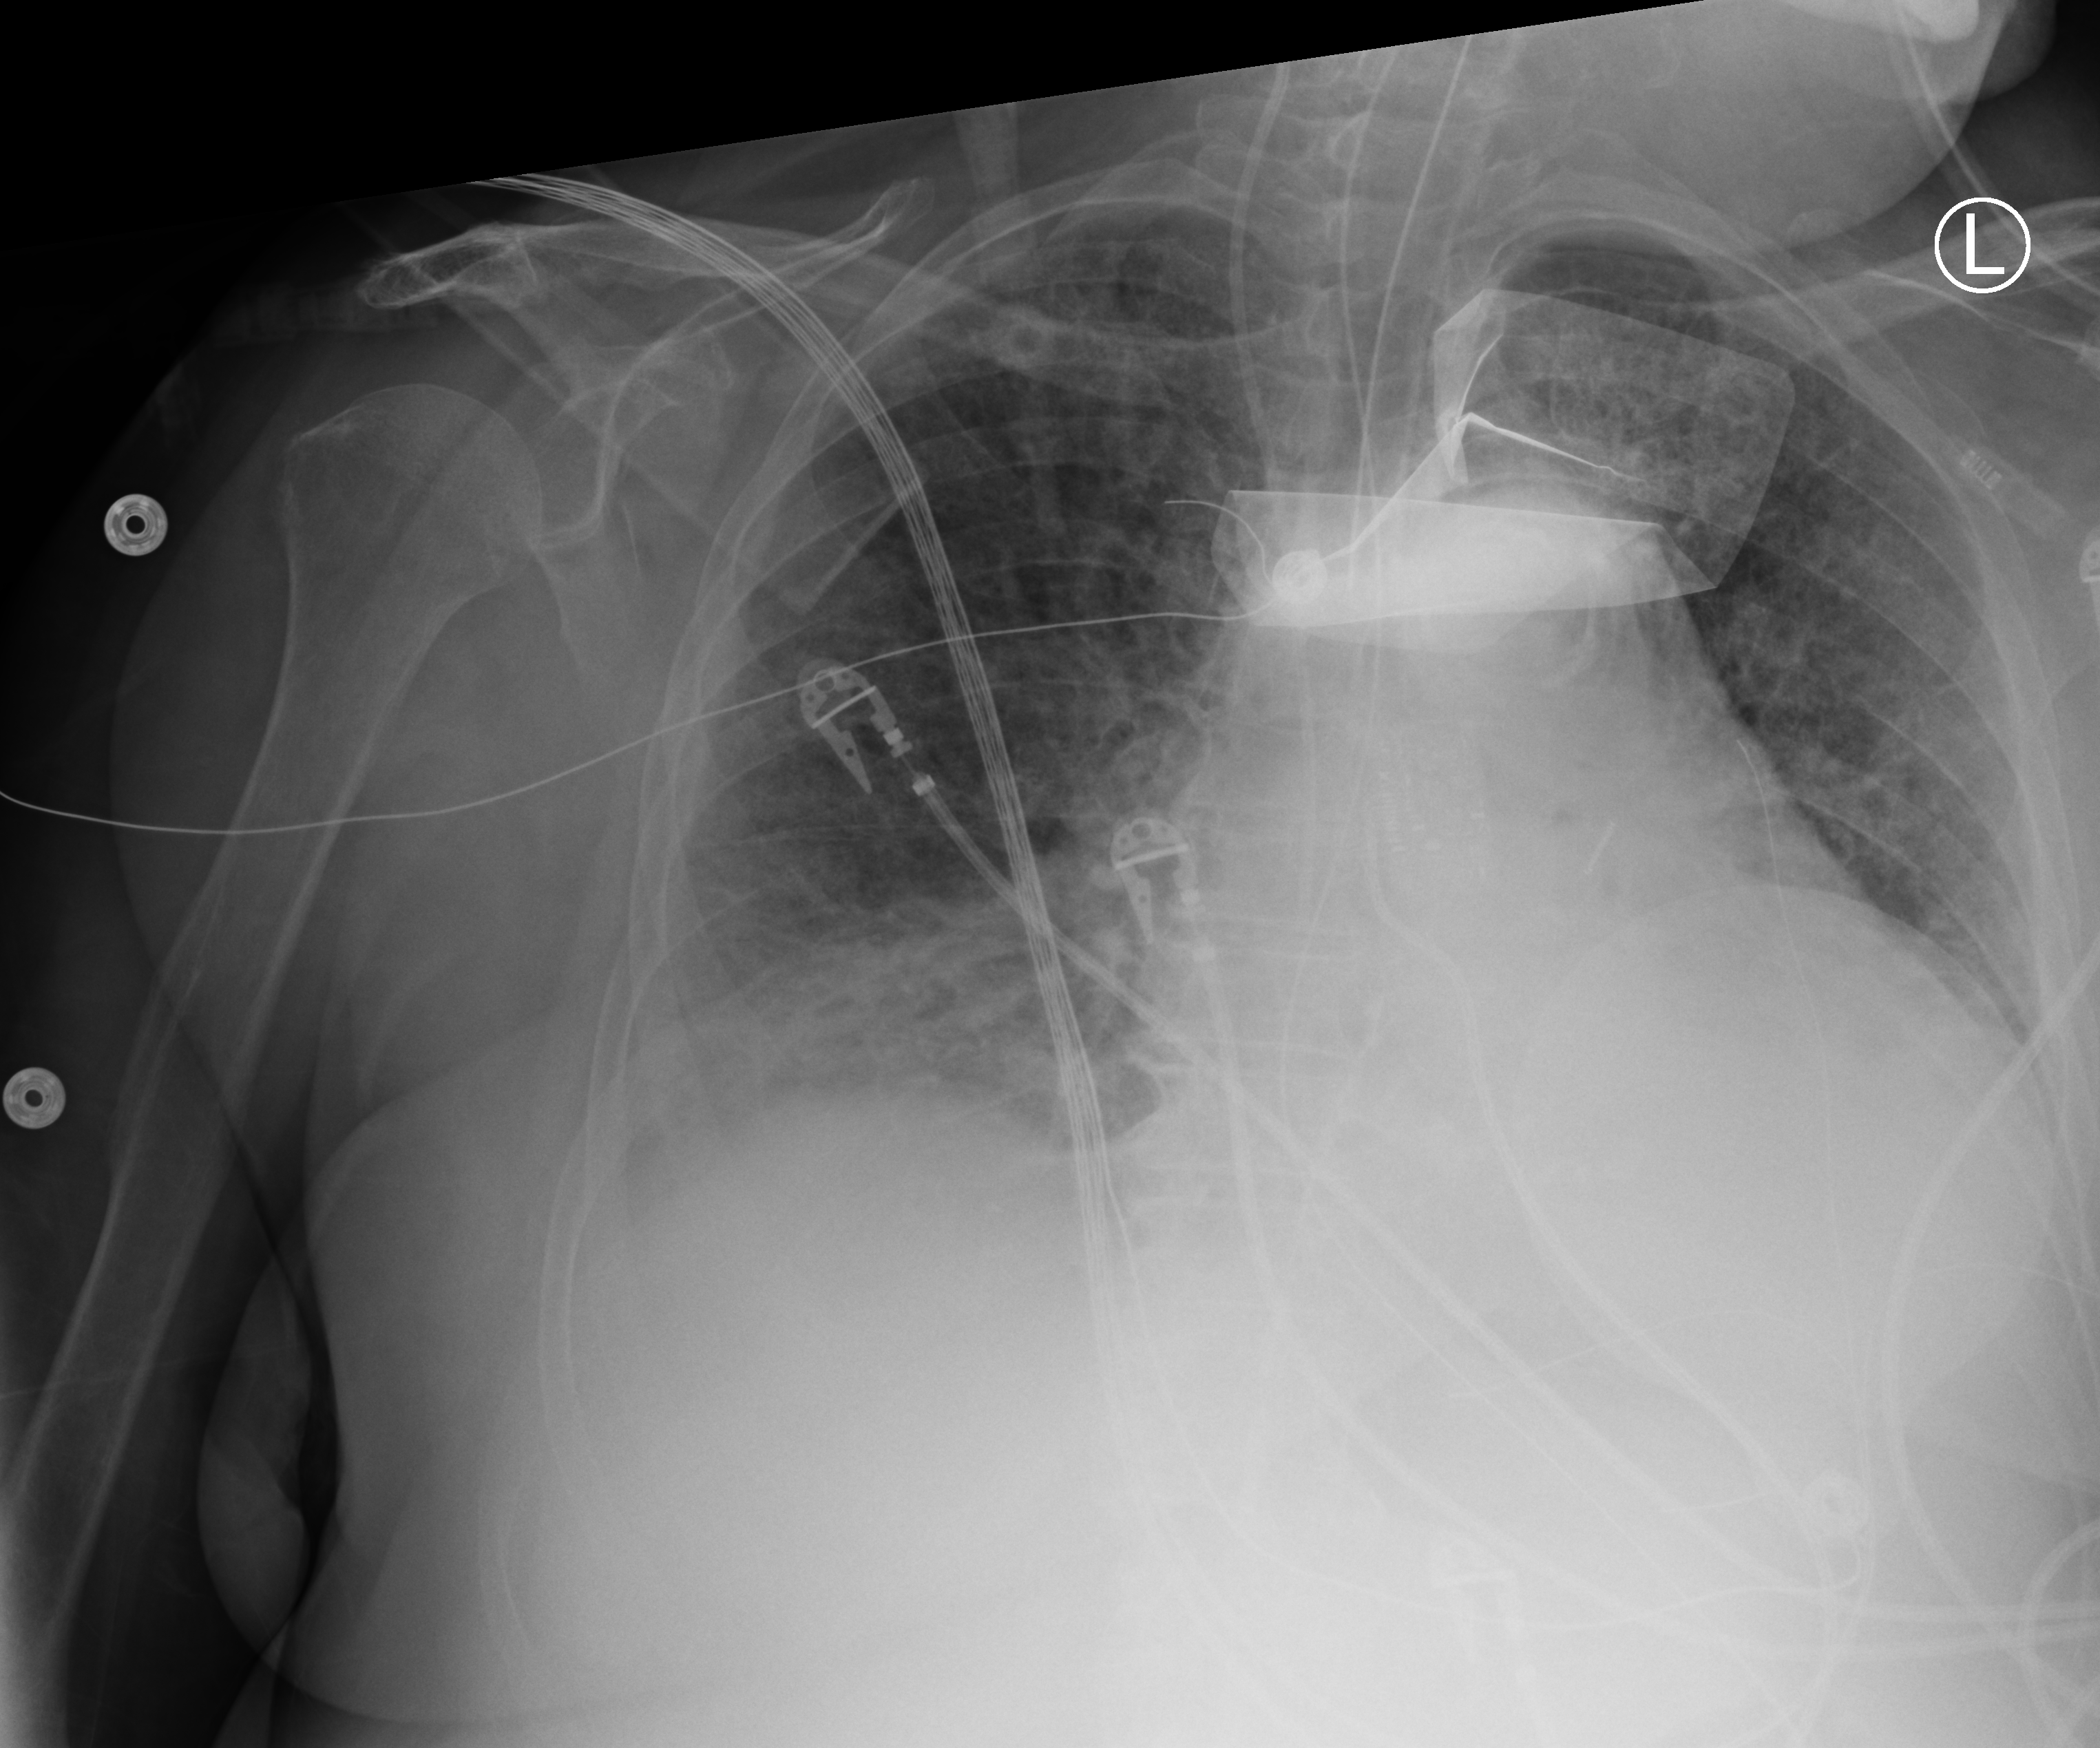
Bedside chest radiograph (computed radiography). Patient hospitalised with COVID-19; female, aged 75–90 years.
From the hospital-stay record, not from the radiograph (when in the stay this image was taken is not recorded):
- COPD (admission record): yes
- mechanically ventilated during this hospital stay: yes
- other chronic lung disease (admission record): no